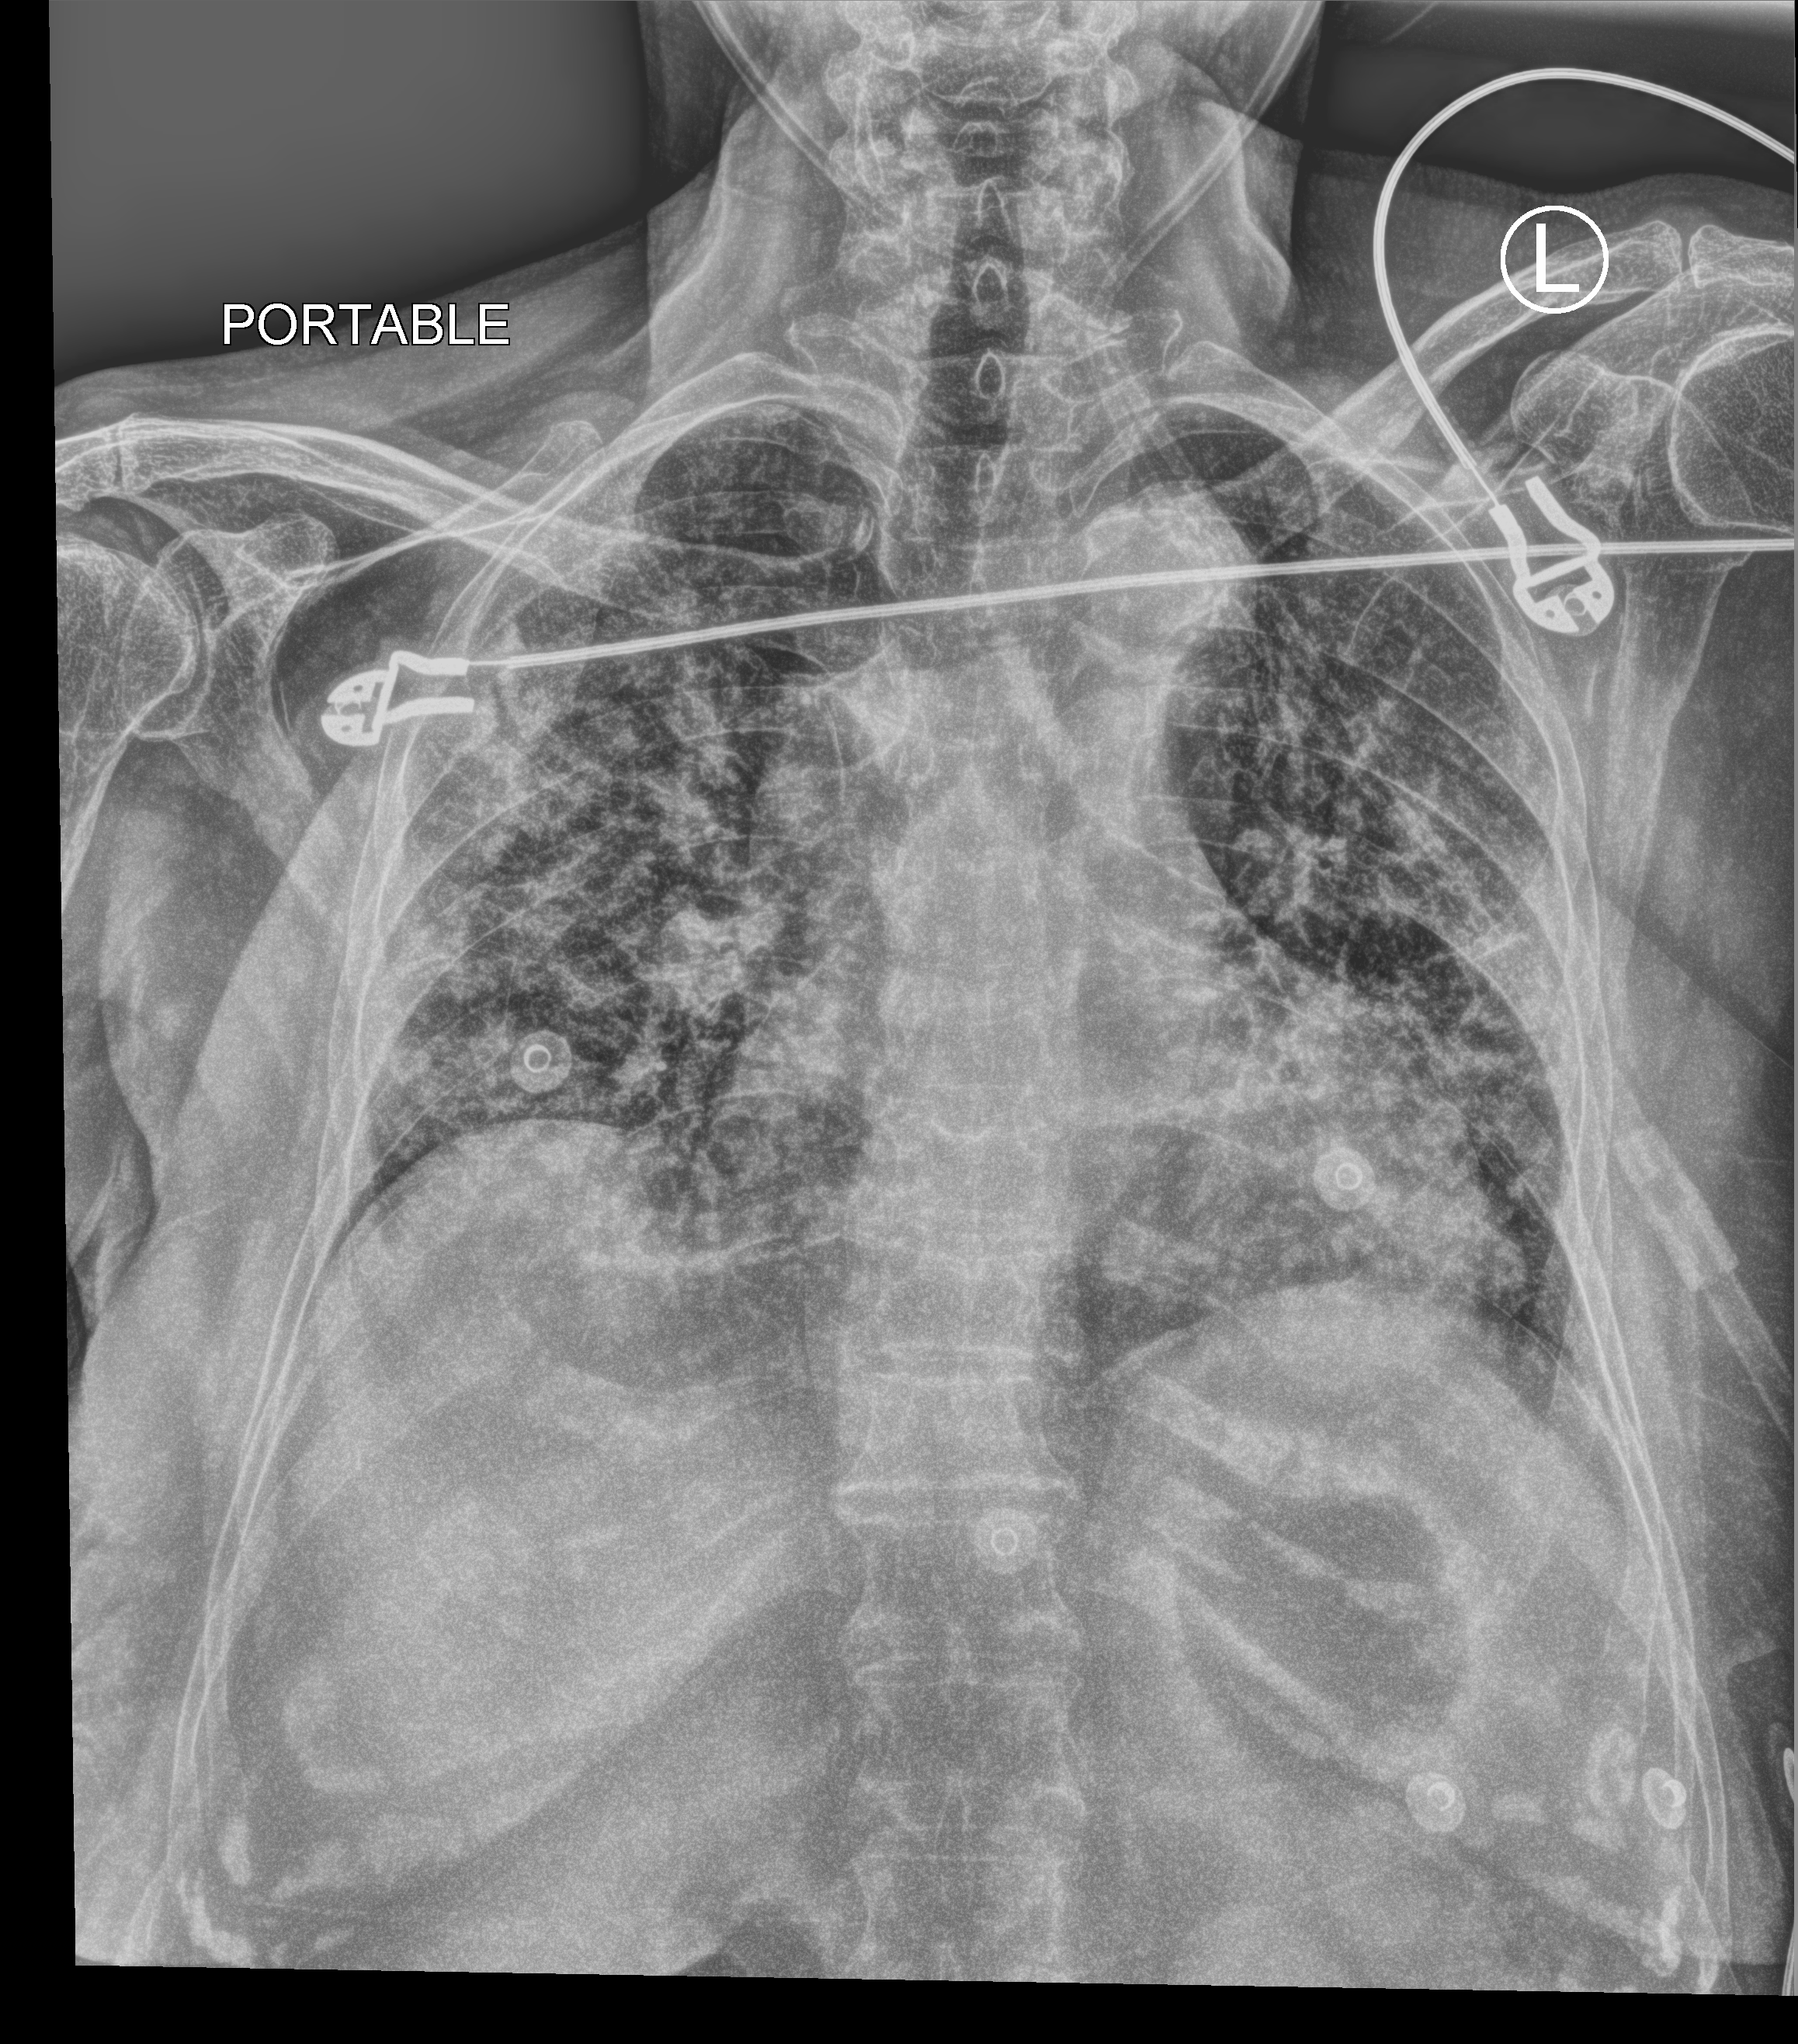
Bedside chest radiograph (computed radiography), anteroposterior (AP) projection. Female patient hospitalised with COVID-19, age 75–90 years.
Admission-level facts for this patient (not findings on this image; timing relative to this image not recorded):
- chronic kidney disease (admission record): no
- mechanically ventilated during this hospital stay: no
- hypertension (admission record): yes